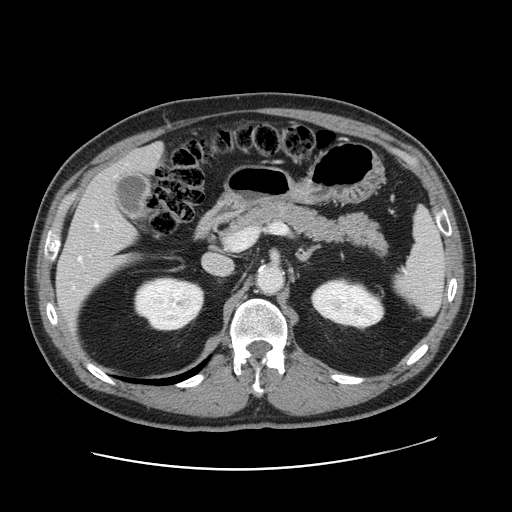
Contrast-enhanced abdominal CT, one axial slice; slice 90 of 178 in the series (ordered by position); 120 kVp; intravenous contrast given; soft-tissue window (W 400 / L 40 HU); 512 × 512 image matrix. Male patient, age 63 years. From the clinical record (not read from this slice): diagnosis: colorectal cancer liver metastases, imaged before liver resection.
Structures marked on this image (manually delineated by an expert):
- hepatic veins: bounding box [x1, y1, x2, y2] px = [79, 223, 98, 260]
- liver: [57, 146, 163, 323]
- planned liver remnant (the part of the liver to remain after resection): [115, 145, 163, 174]